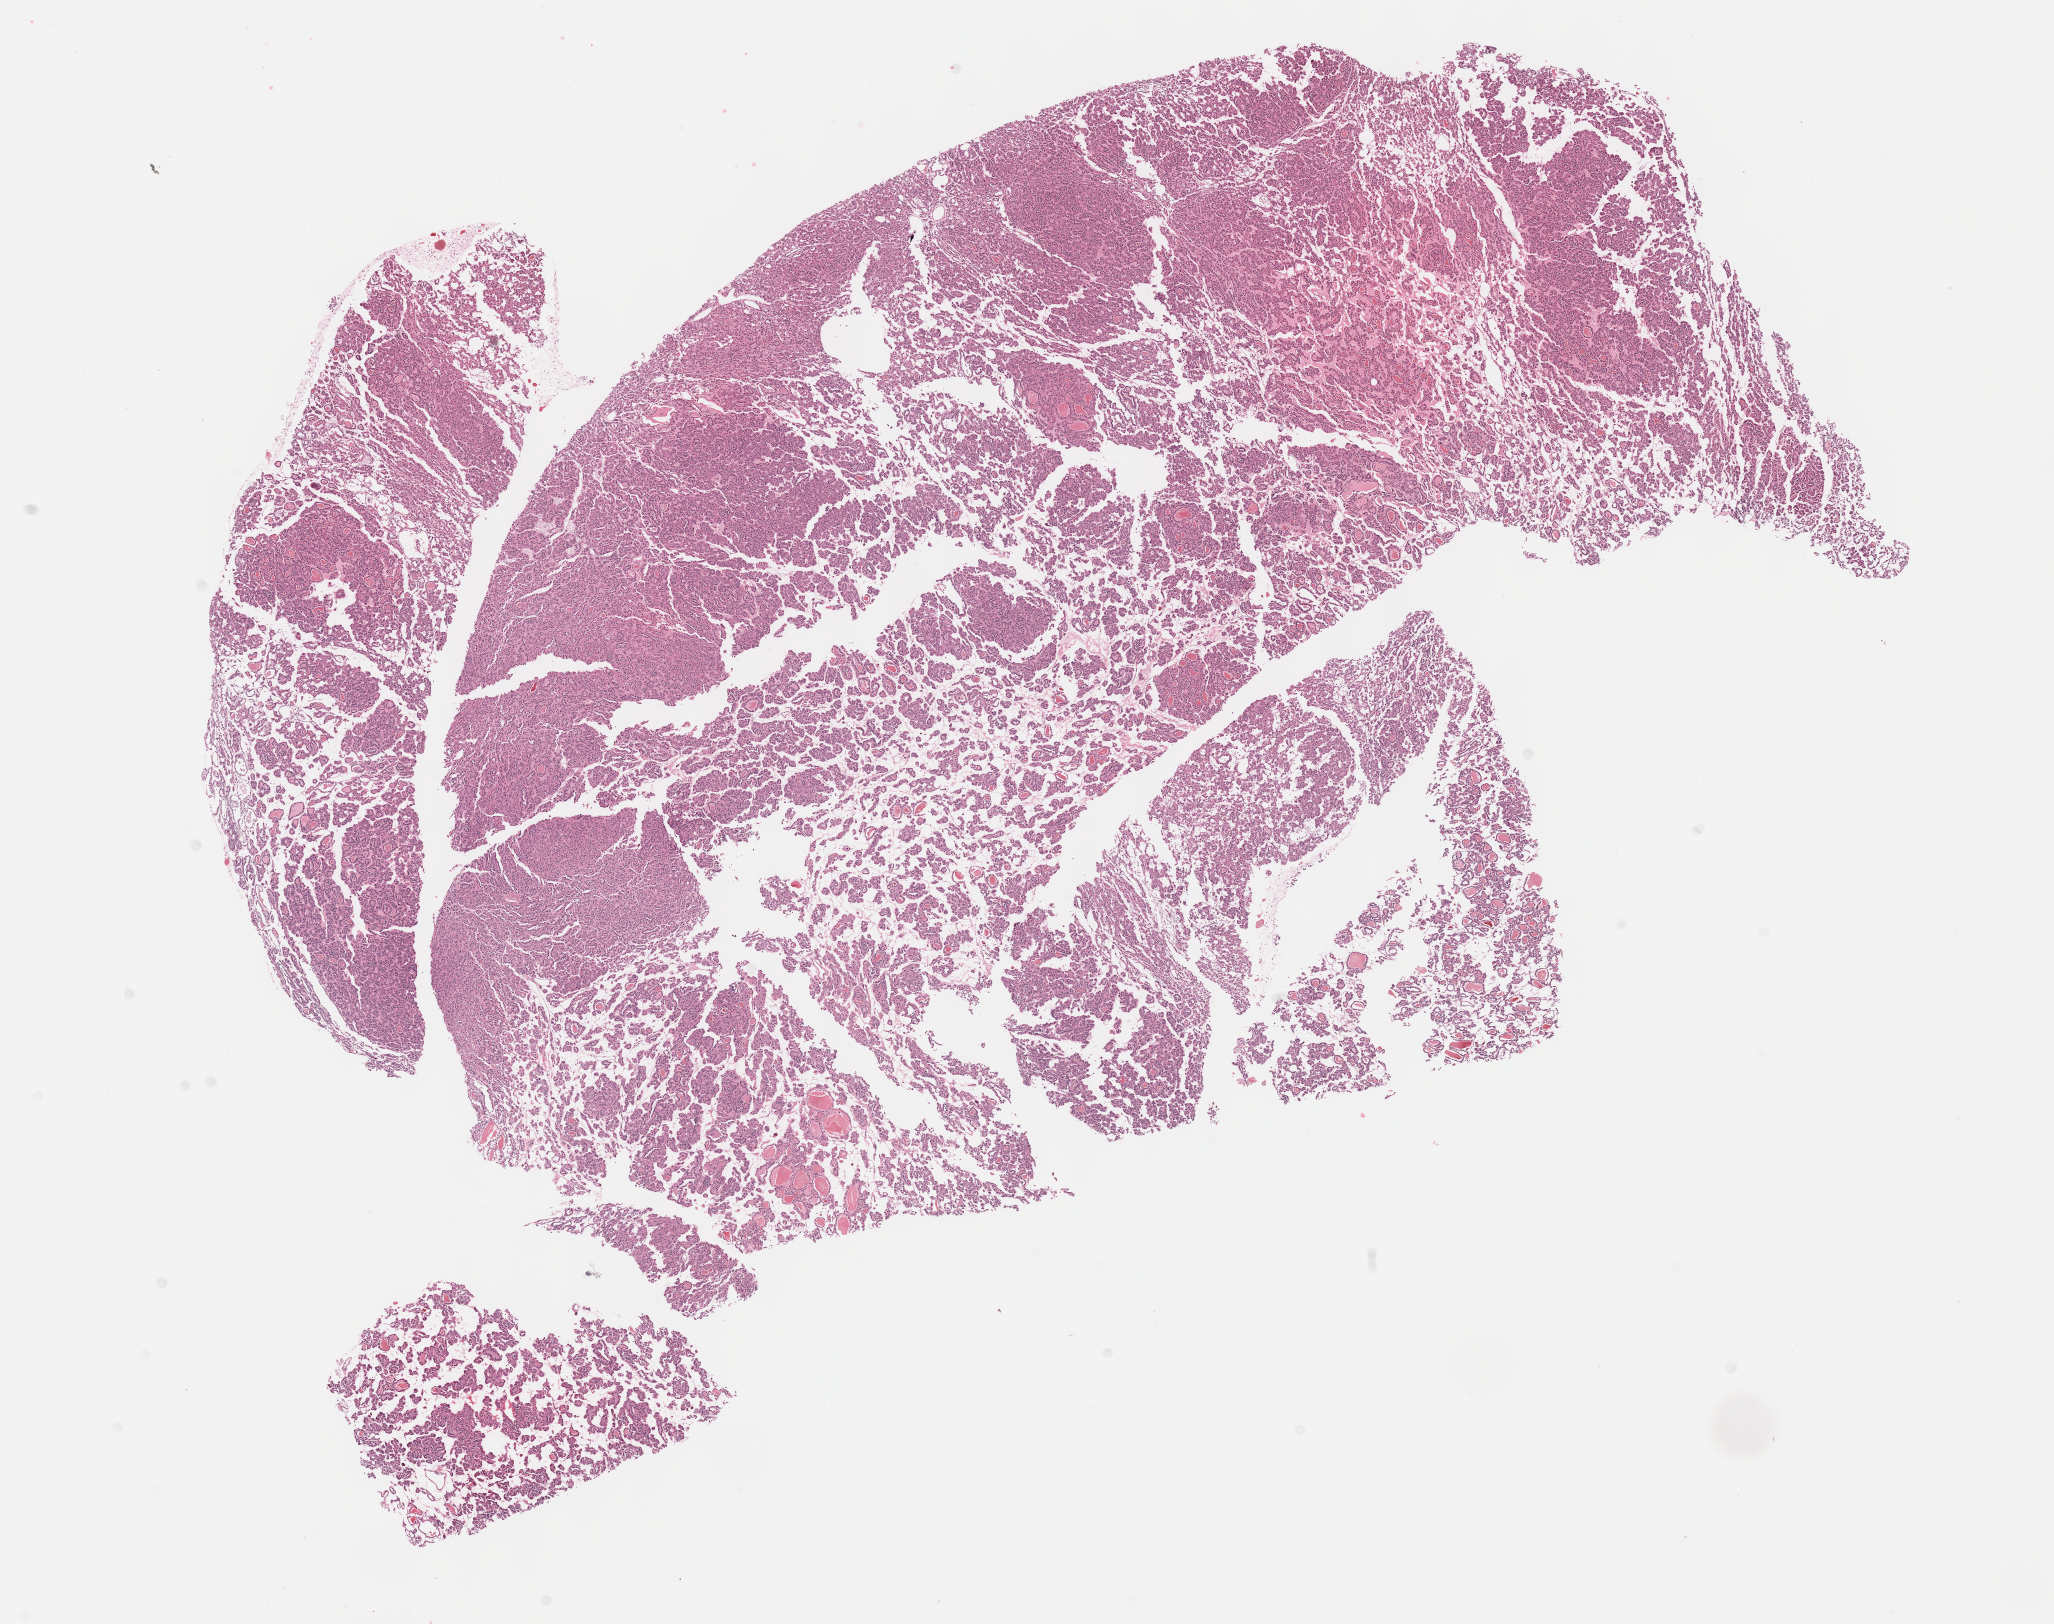
H&E-stained whole-slide image — low-resolution overview of the scanned area, about 16.6 x 13.1 mm. Formalin-fixed paraffin-embedded (FFPE) diagnostic section. Primary tumour sample from the kidney. Patient: female, age at initial diagnosis 58 years. Histologic grade: G2 (moderately differentiated).
Laterality: right. AJCC pathologic stage: II (6th edition). Pathologic diagnosis: Clear cell adenocarcinoma, NOS.